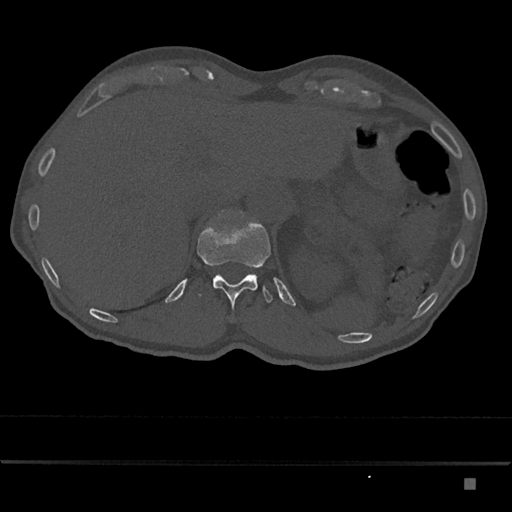
CT including the spine, one axial slice. Position 608 of 797 along the scan axis. Reconstruction kernel Br40s/3. 120 kVp. Bone window (W 1800 / L 400 HU). 0.5 mm slice thickness. 512 × 512 image matrix. Patient: male, 72 years. From the clinical record (not read from this slice): primary cancer: prostate.
Outlined on this slice (semi-automatically segmented with operator editing):
- T12 vertebra: bounding box (x1, y1, x2, y2) in pixels: (197, 221, 273, 311)